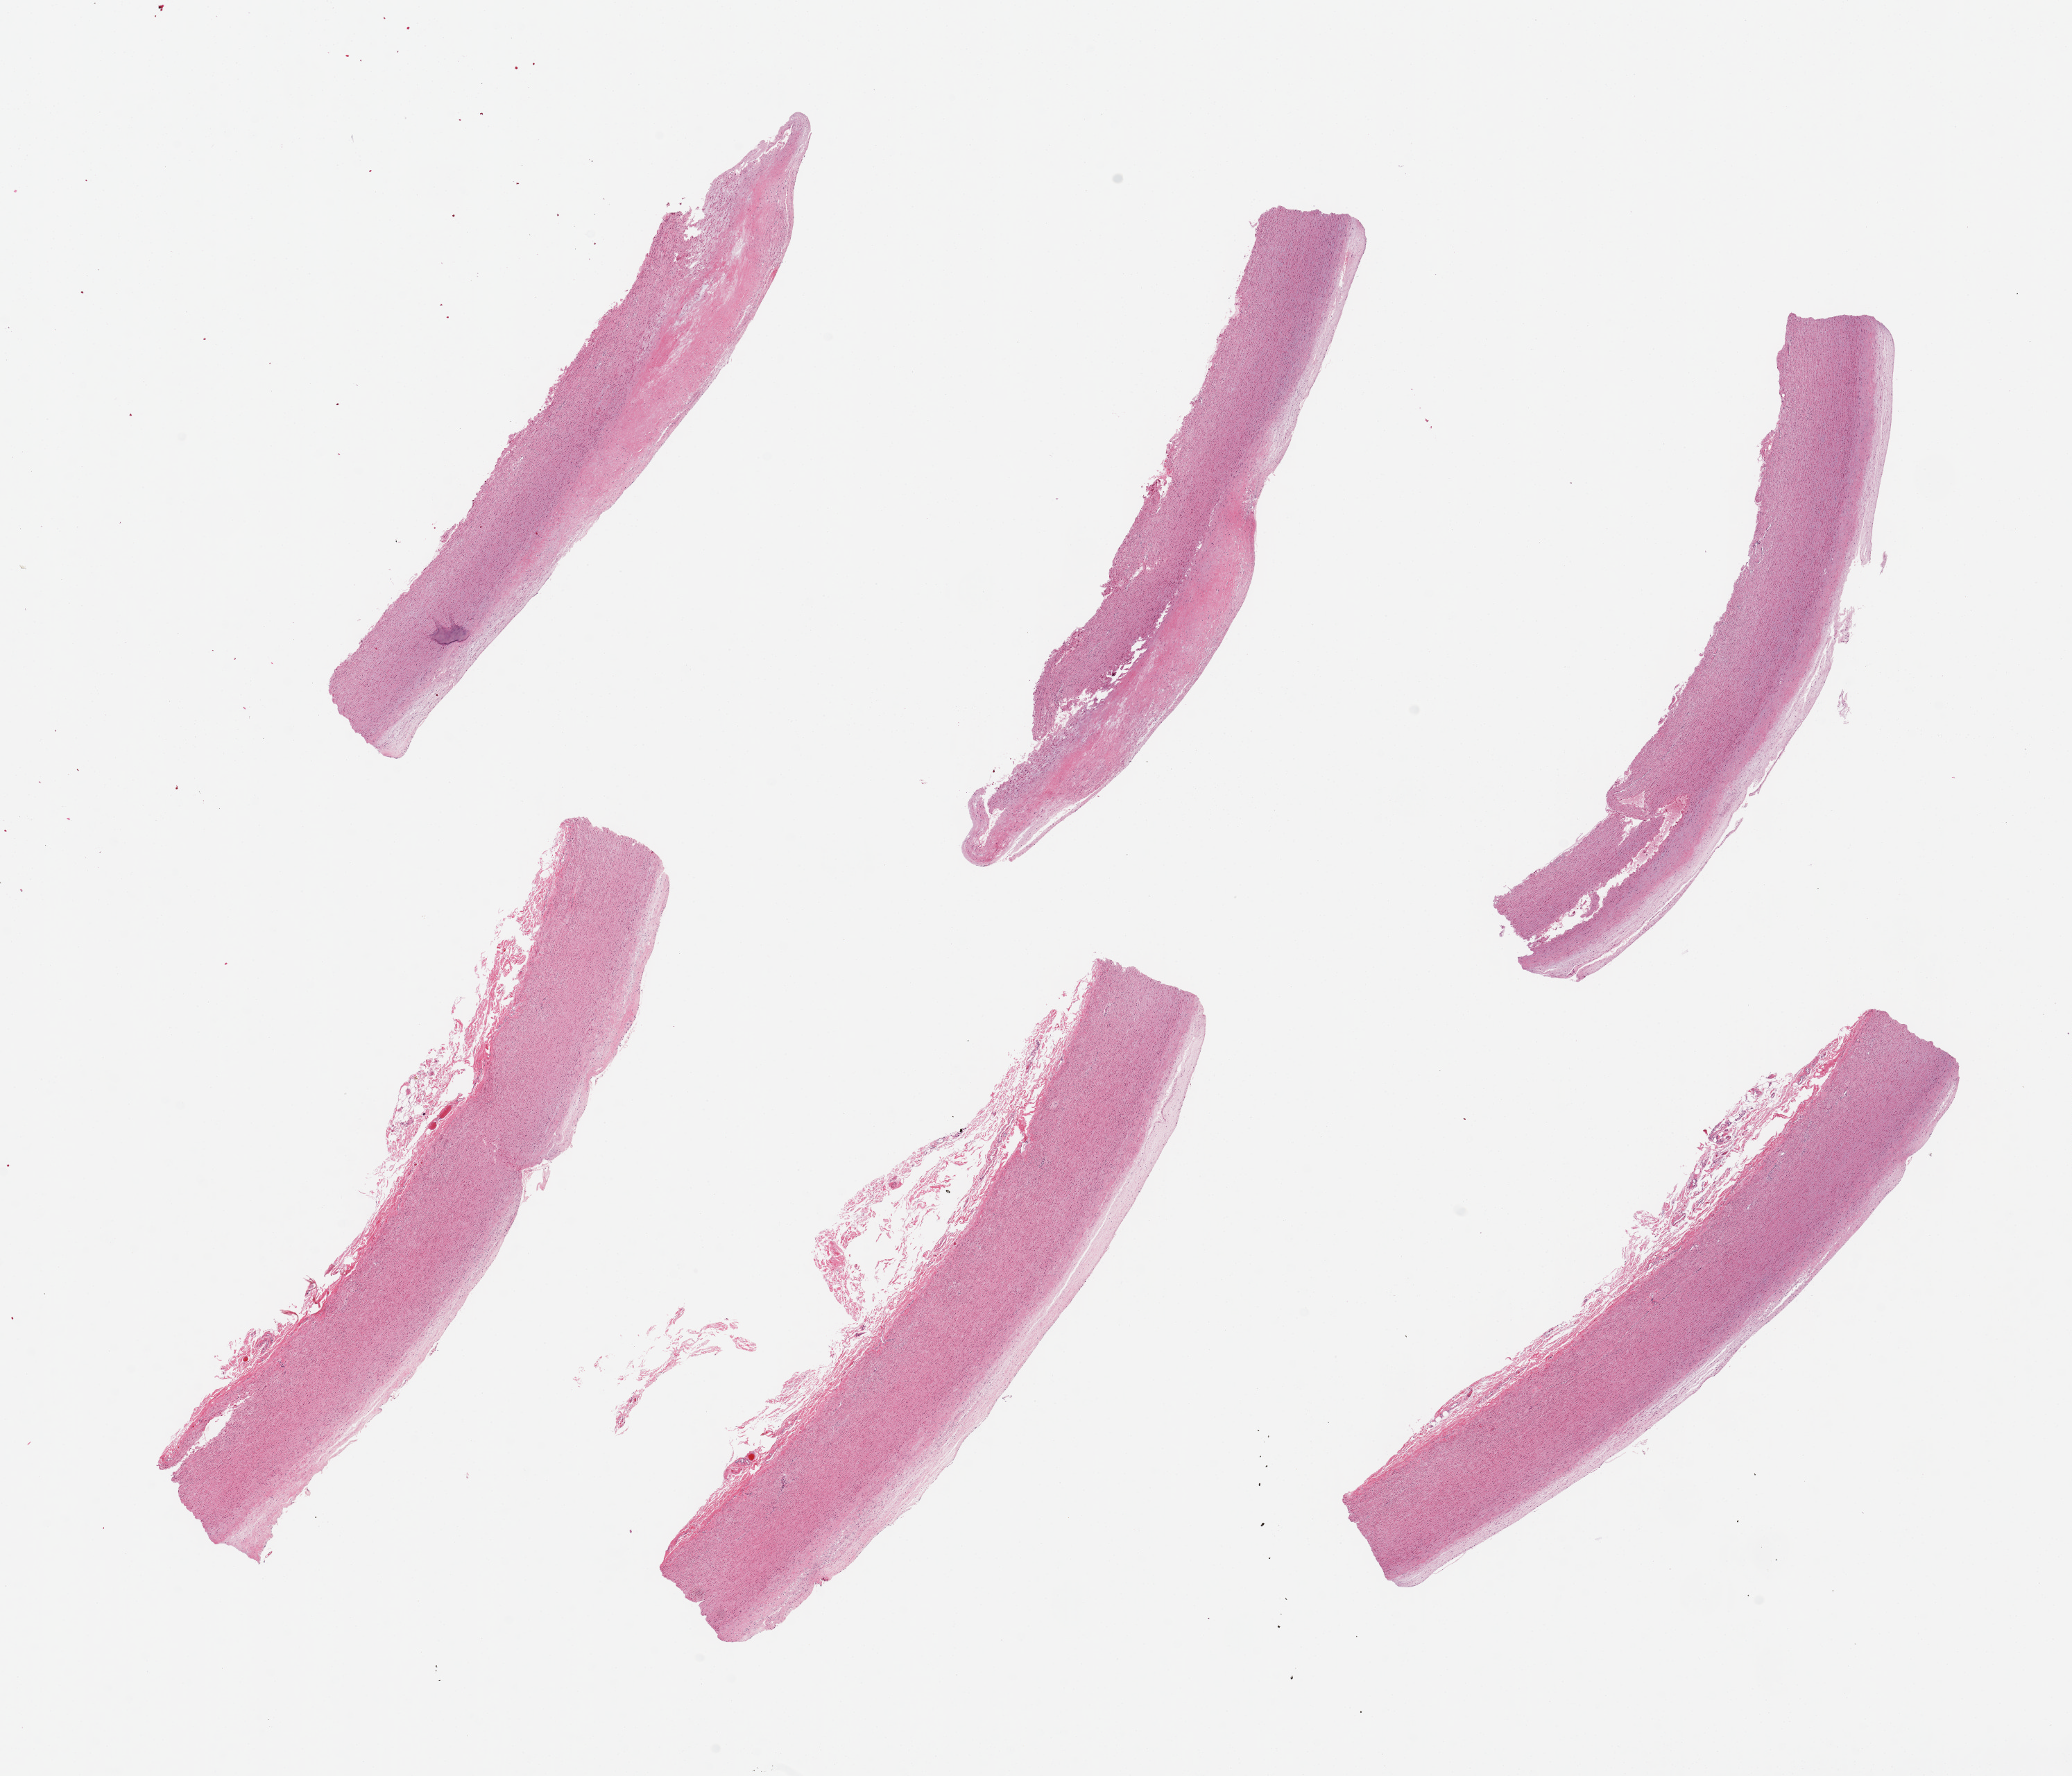
Whole-slide image, hematoxylin and eosin (H&E) stain — shown as a low-resolution overview of the whole scanned area (about 23.6 x 20.2 mm). PAXgene-fixed, paraffin-embedded tissue. Section of aorta (target tissue). Donor tissue sample. Male donor.
- reviewer comment on this tissue sample: 6 pieces, up to 9x2mm; flat plaques; focal medial dissections